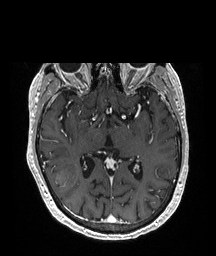
Brain MRI from a brain-tumour surgery series, one axial slice; slice 116 of 208 in the series (ordered by position); T1-weighted post-contrast; 216 × 256 image matrix, field of view 216 × 256 mm. From the clinical record (not read from this slice): histopathology: Glioblastoma; WHO grade: 4; IDH mutation: no.
Outlined on this slice (outlined manually by an expert reader):
- tumour: bounding box (x1, y1, x2, y2) in pixels: (48, 158, 77, 190)